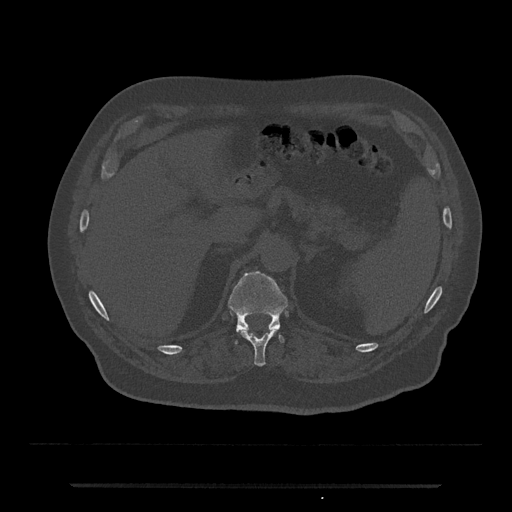
CT including the spine, one axial slice; slice 619 of 797 in the series (ordered by position); bone window (W 1800 / L 400 HU); 0.5 mm slice thickness; 512 × 512 image matrix, field of view 434 × 434 mm. Male patient, age 80 years. From the clinical record (not read from this slice): primary cancer: prostate; vertebrae with lytic lesions (as recorded): L1, T11.
Structures marked on this image (semi-automatically segmented with operator editing):
- T11 vertebra: bounding box (x1, y1, x2, y2) in pixels: (240, 329, 277, 366)
- T12 vertebra: (228, 270, 288, 345)